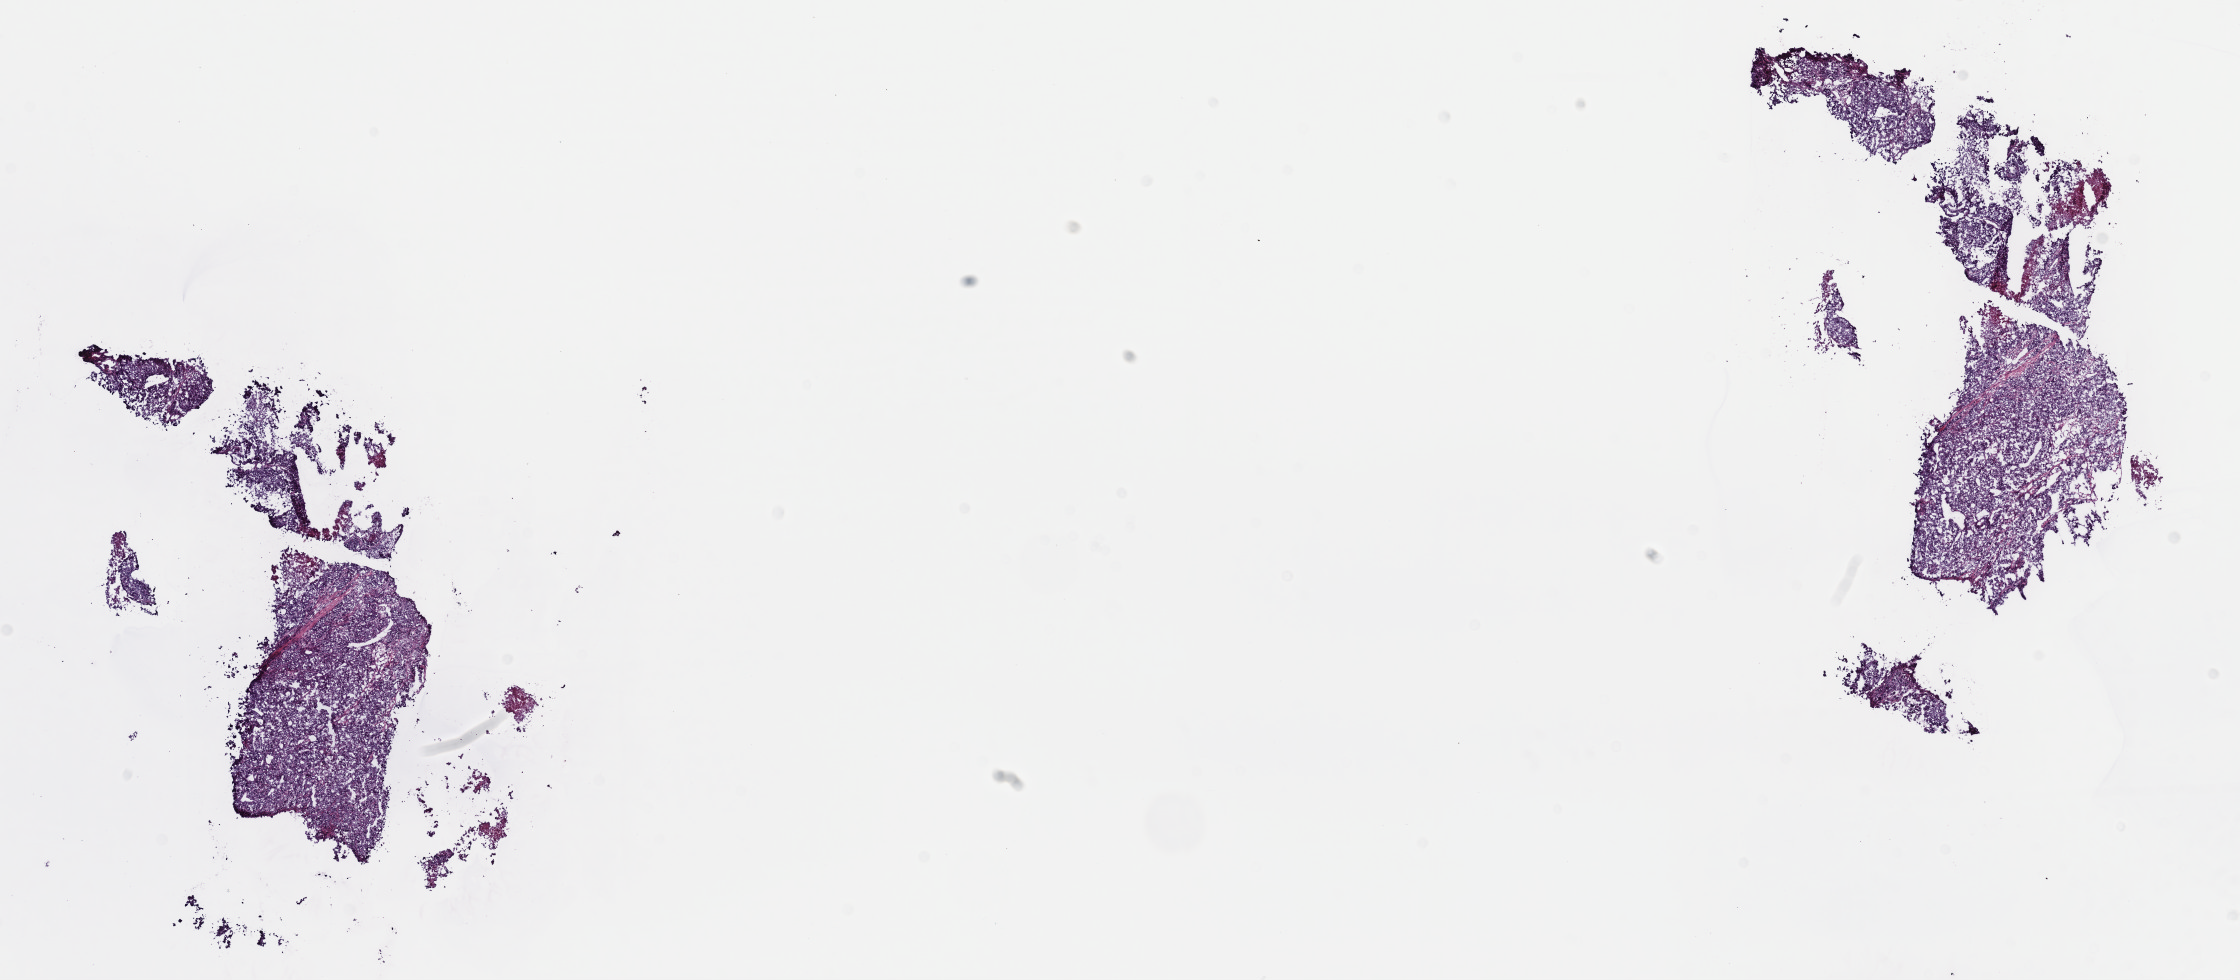
Whole-slide histology image, Hematoxylin and eosin (H&E) stained, whole scanned area (about 18.1 x 7.9 mm) shown as a low-resolution overview, frozen section from the top of the tissue portion, primary tumour sample from the liver. Male patient; age at initial diagnosis 38 years. Histologic grade: G2 (moderately differentiated). Pathologist review of this section (percent, as recorded): tumour cells 88%, tumour nuclei 95%, normal cells 0%, stromal cells 2%, necrosis 10%. Inflammatory infiltration, as recorded: lymphocyte infiltration 0%, monocyte infiltration 0%, neutrophil infiltration 0%.
AJCC pathologic stage: II (7th edition). Histologic diagnosis: Hepatocellular carcinoma, NOS.